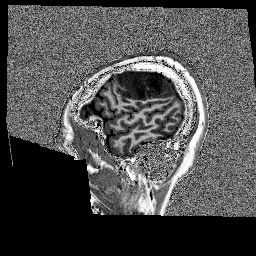
Brain MRI from a brain-tumour surgery series, one sagittal slice. Position 34 of 176 along the scan axis. 1 mm slice thickness. 256 × 256 image matrix, field of view 256 × 256 mm. Case-level facts recorded for this patient, not image findings: histopathology: Glioblastoma; WHO grade: 4; IDH mutation: no; tumour location: Left Frontal.
Annotated regions visible in this slice (outlined manually by an expert reader):
- tumour: box from (x=120, y=71) to (x=175, y=100) px